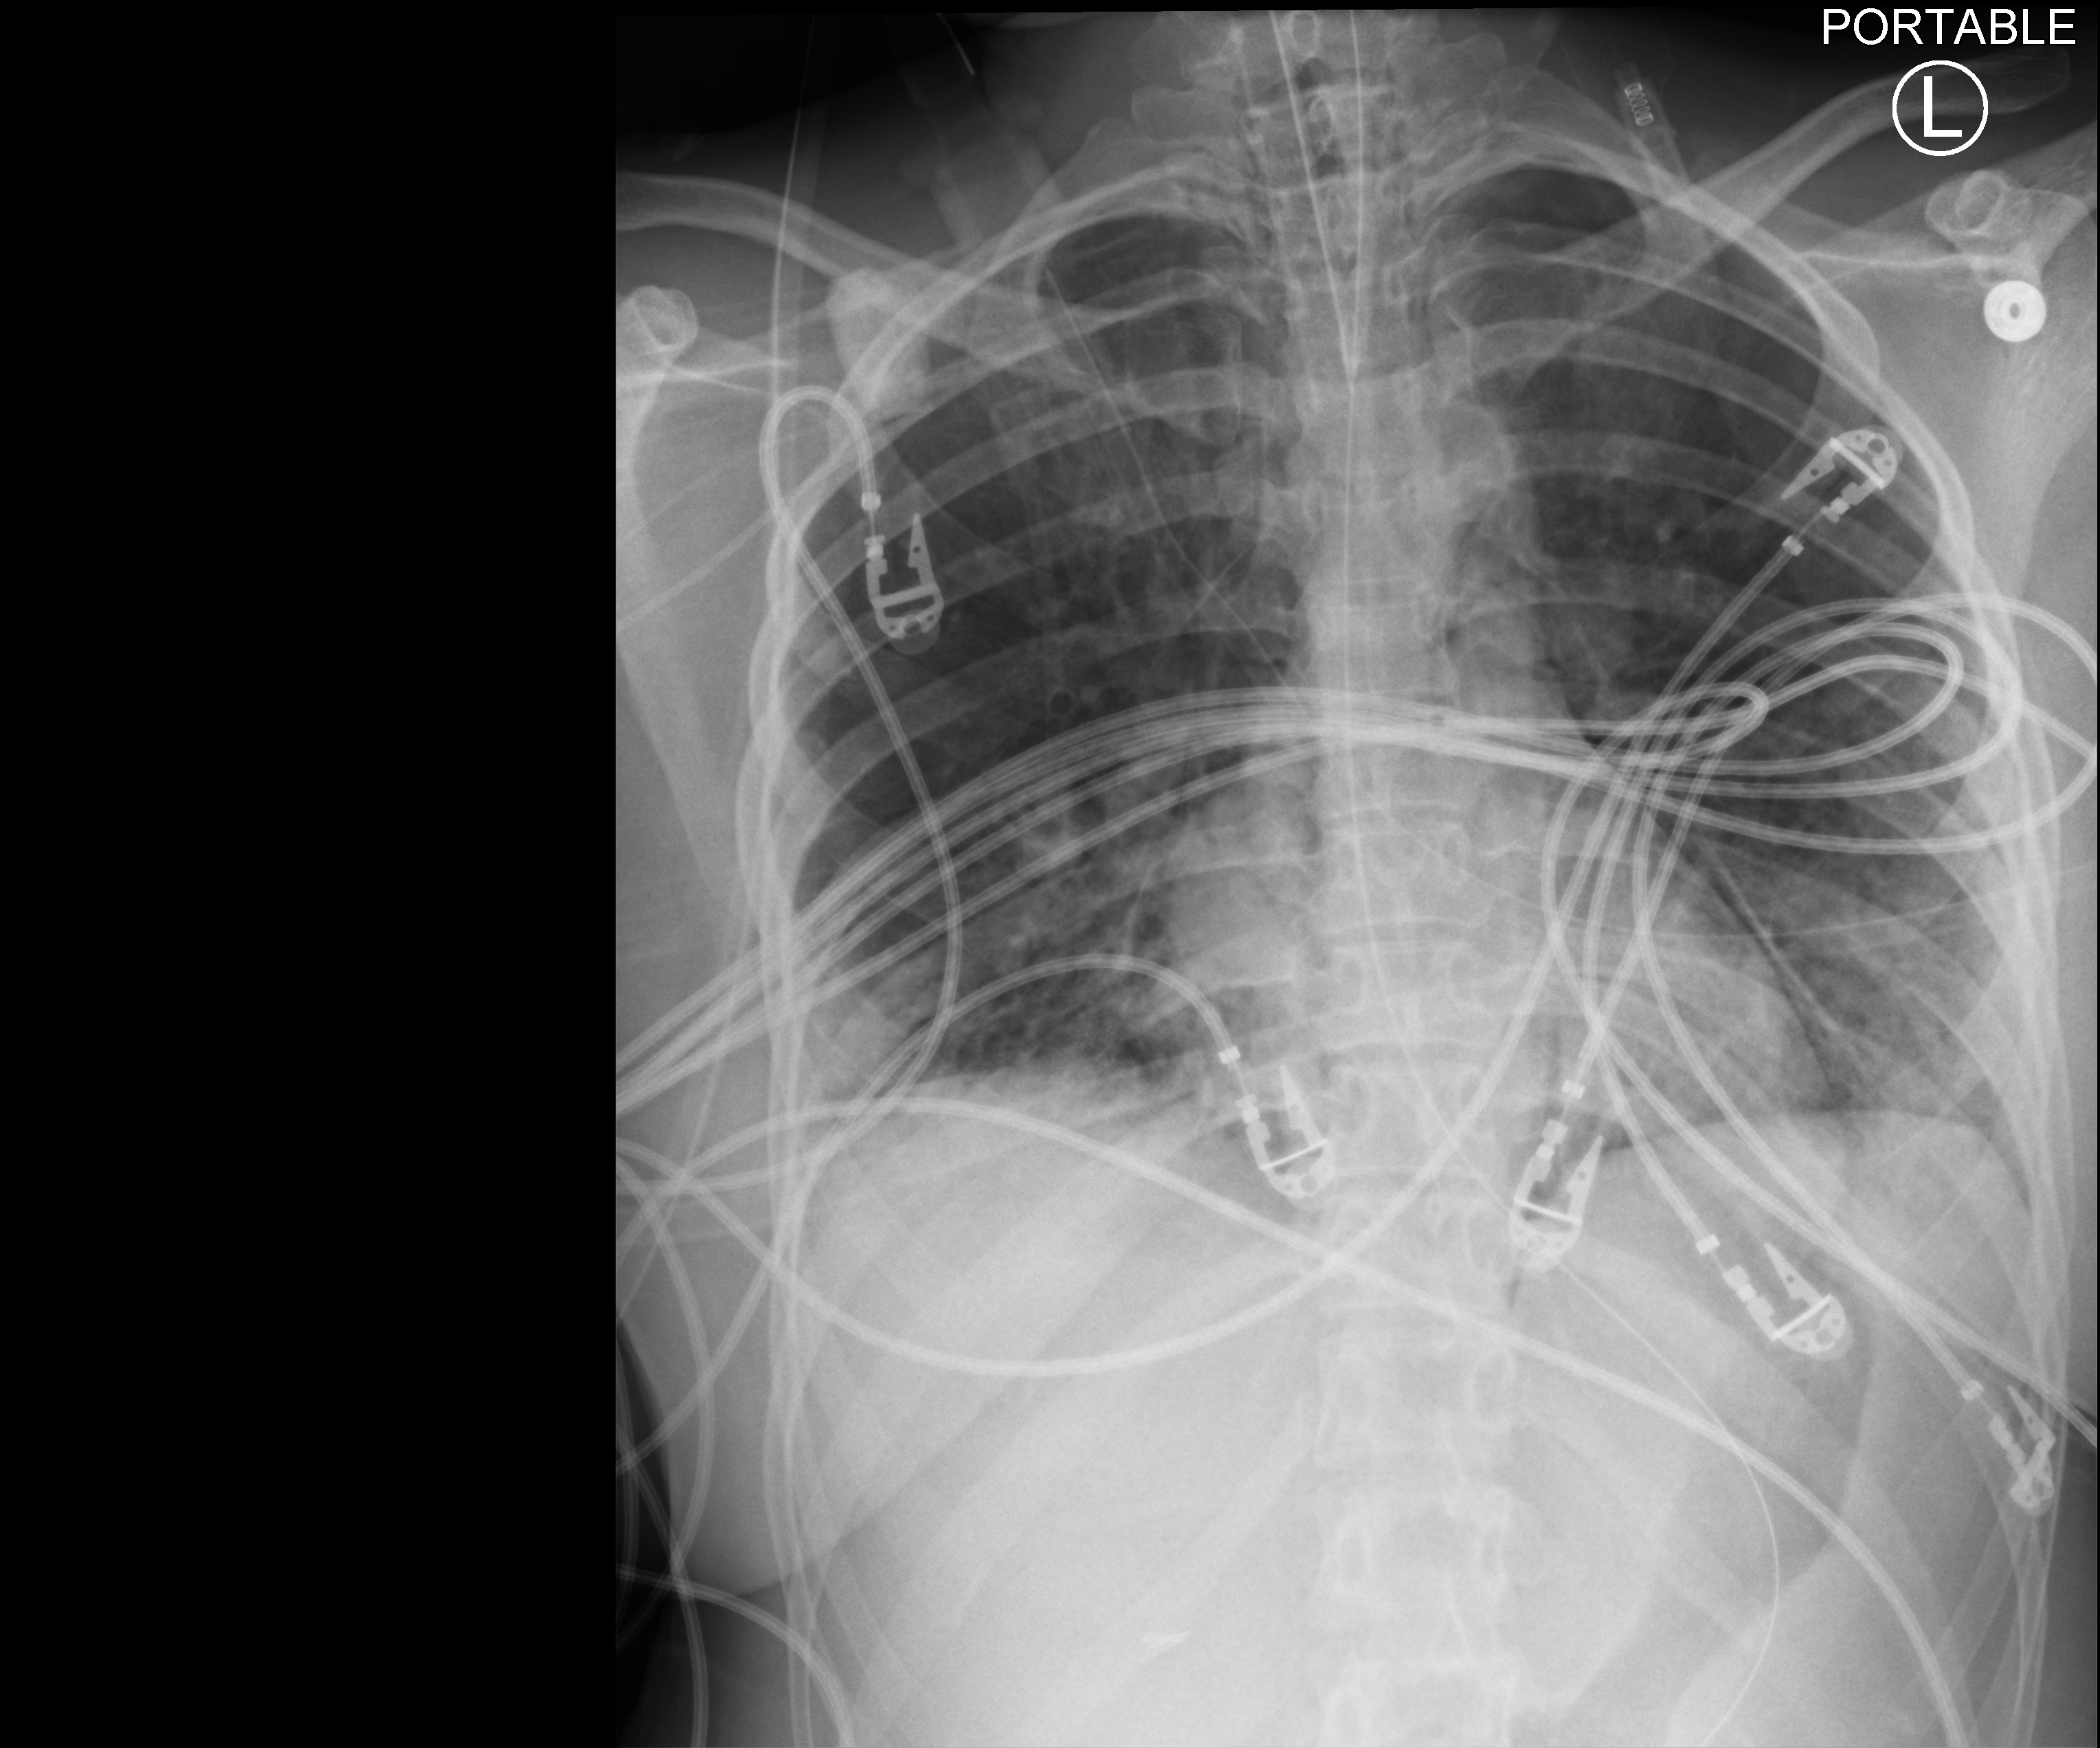
Chest X-ray (portable), anteroposterior (AP) projection. Patient hospitalised with COVID-19, aged 18–59 years.
Hospital-stay facts (about this admission, not read from this image; timing relative to this image not recorded):
- admitted to intensive care during this hospital stay: yes